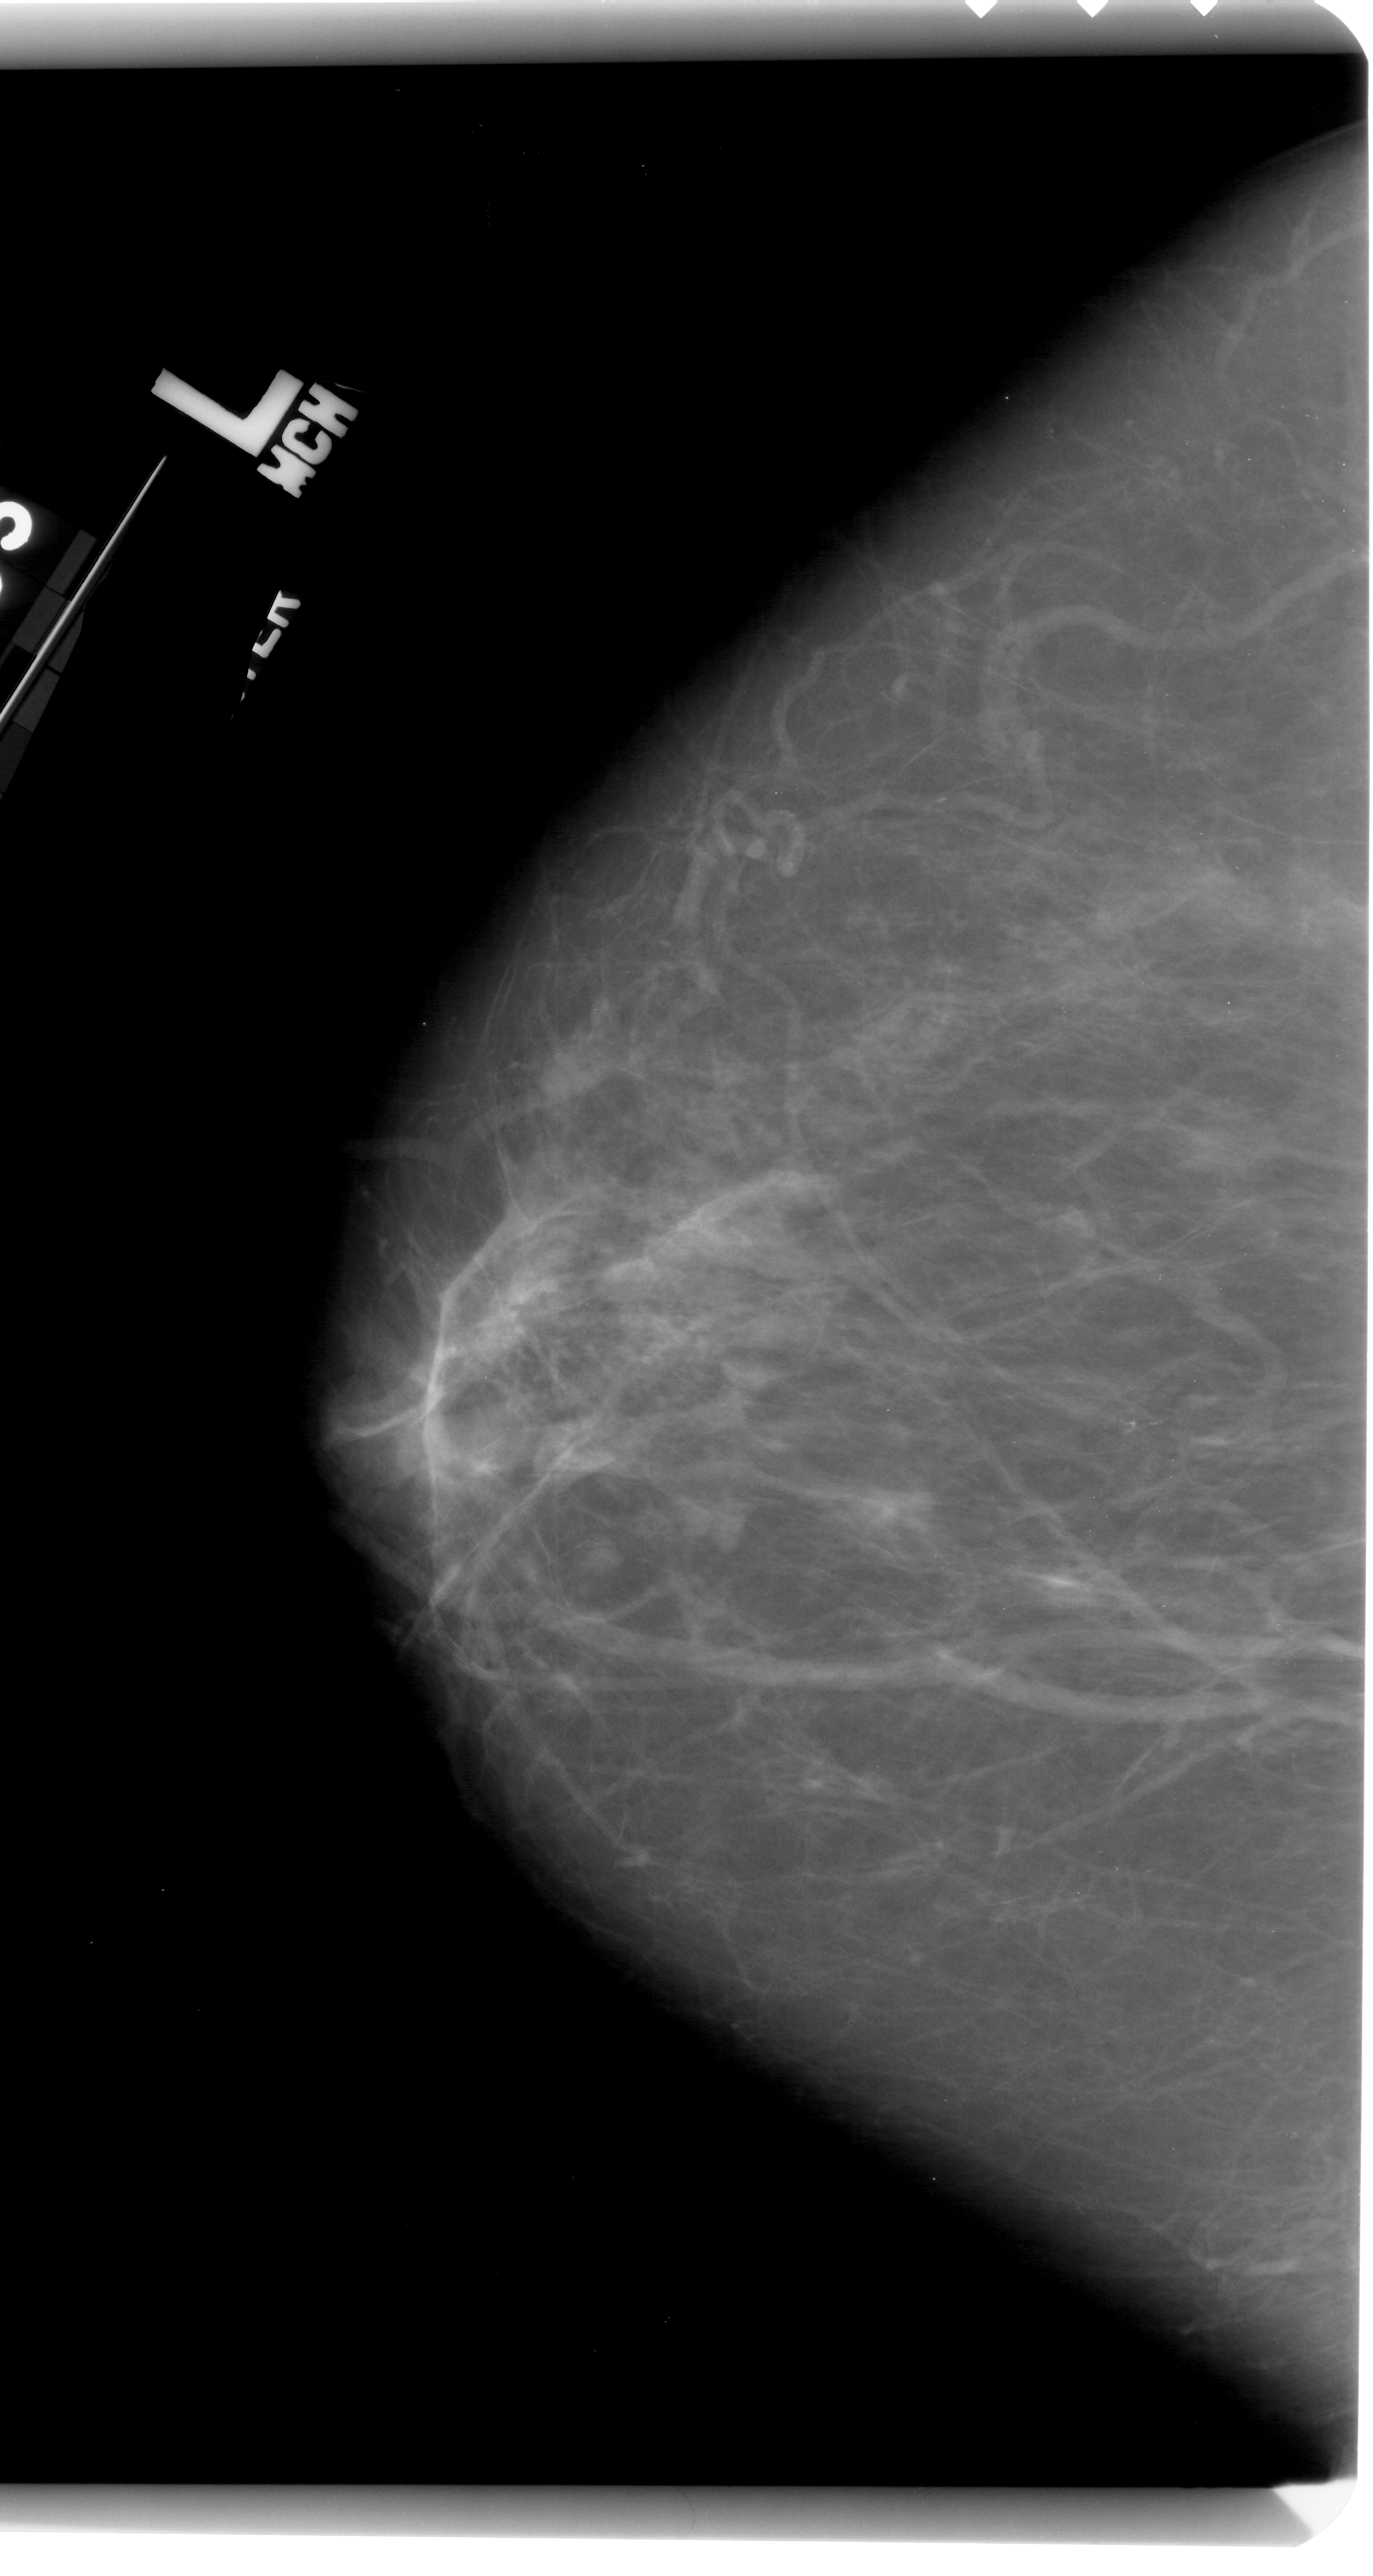
Scanned film-screen mammogram; left breast; craniocaudal (CC) view; breast composition: scattered fibroglandular densities (BI-RADS density category 2 of 4); 1373 × 2576 image matrix.
Expert-marked regions of interest on this film, with their recorded descriptors:
- calcifications, morphology fine linear branching, distribution linear; BI-RADS assessment category 4; pathology (as recorded): malignant: bounding box [x1, y1, x2, y2] px = [1096, 1395, 1217, 1447]